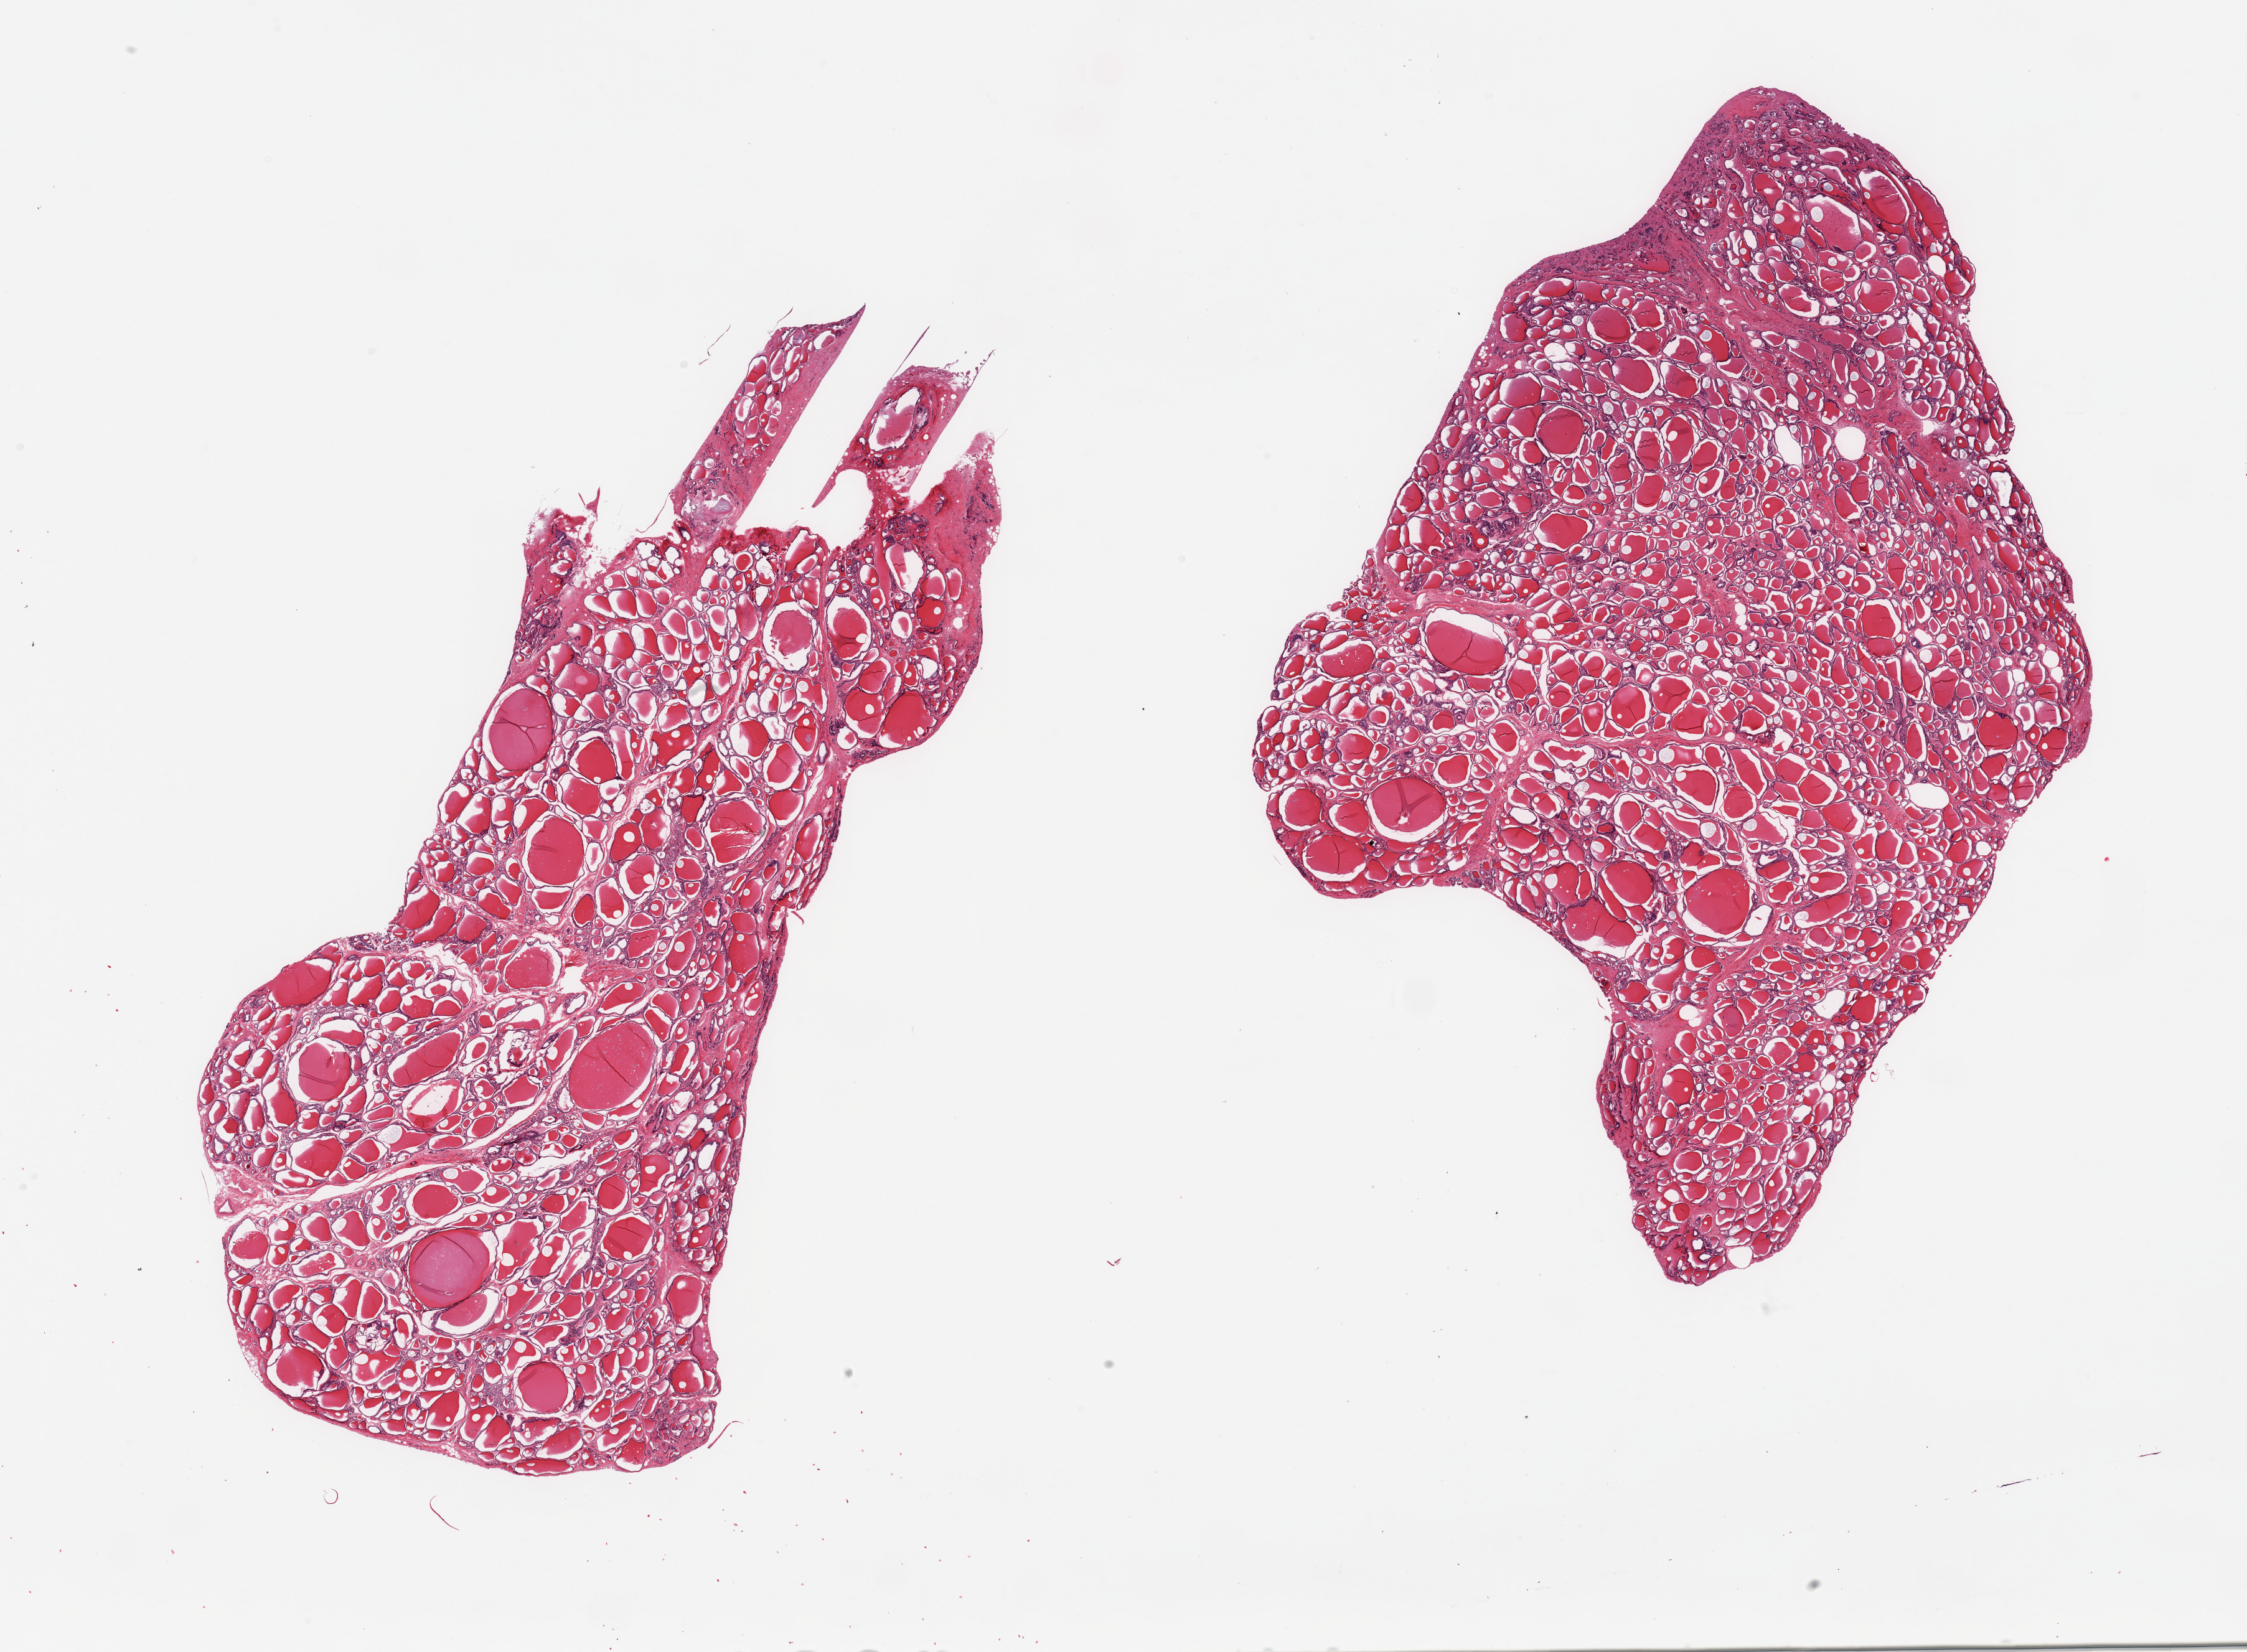
Hematoxylin and eosin (H&E) whole-slide image — low-resolution overview of the scanned area, about 28.5 x 21.0 mm (slide scanned at 20x); PAXgene-fixed paraffin-embedded (PFPE) section; target tissue: thyroid; tissue donor sample. Donor: female.
Review note (as recorded): 2 pieces, no abnormalities.